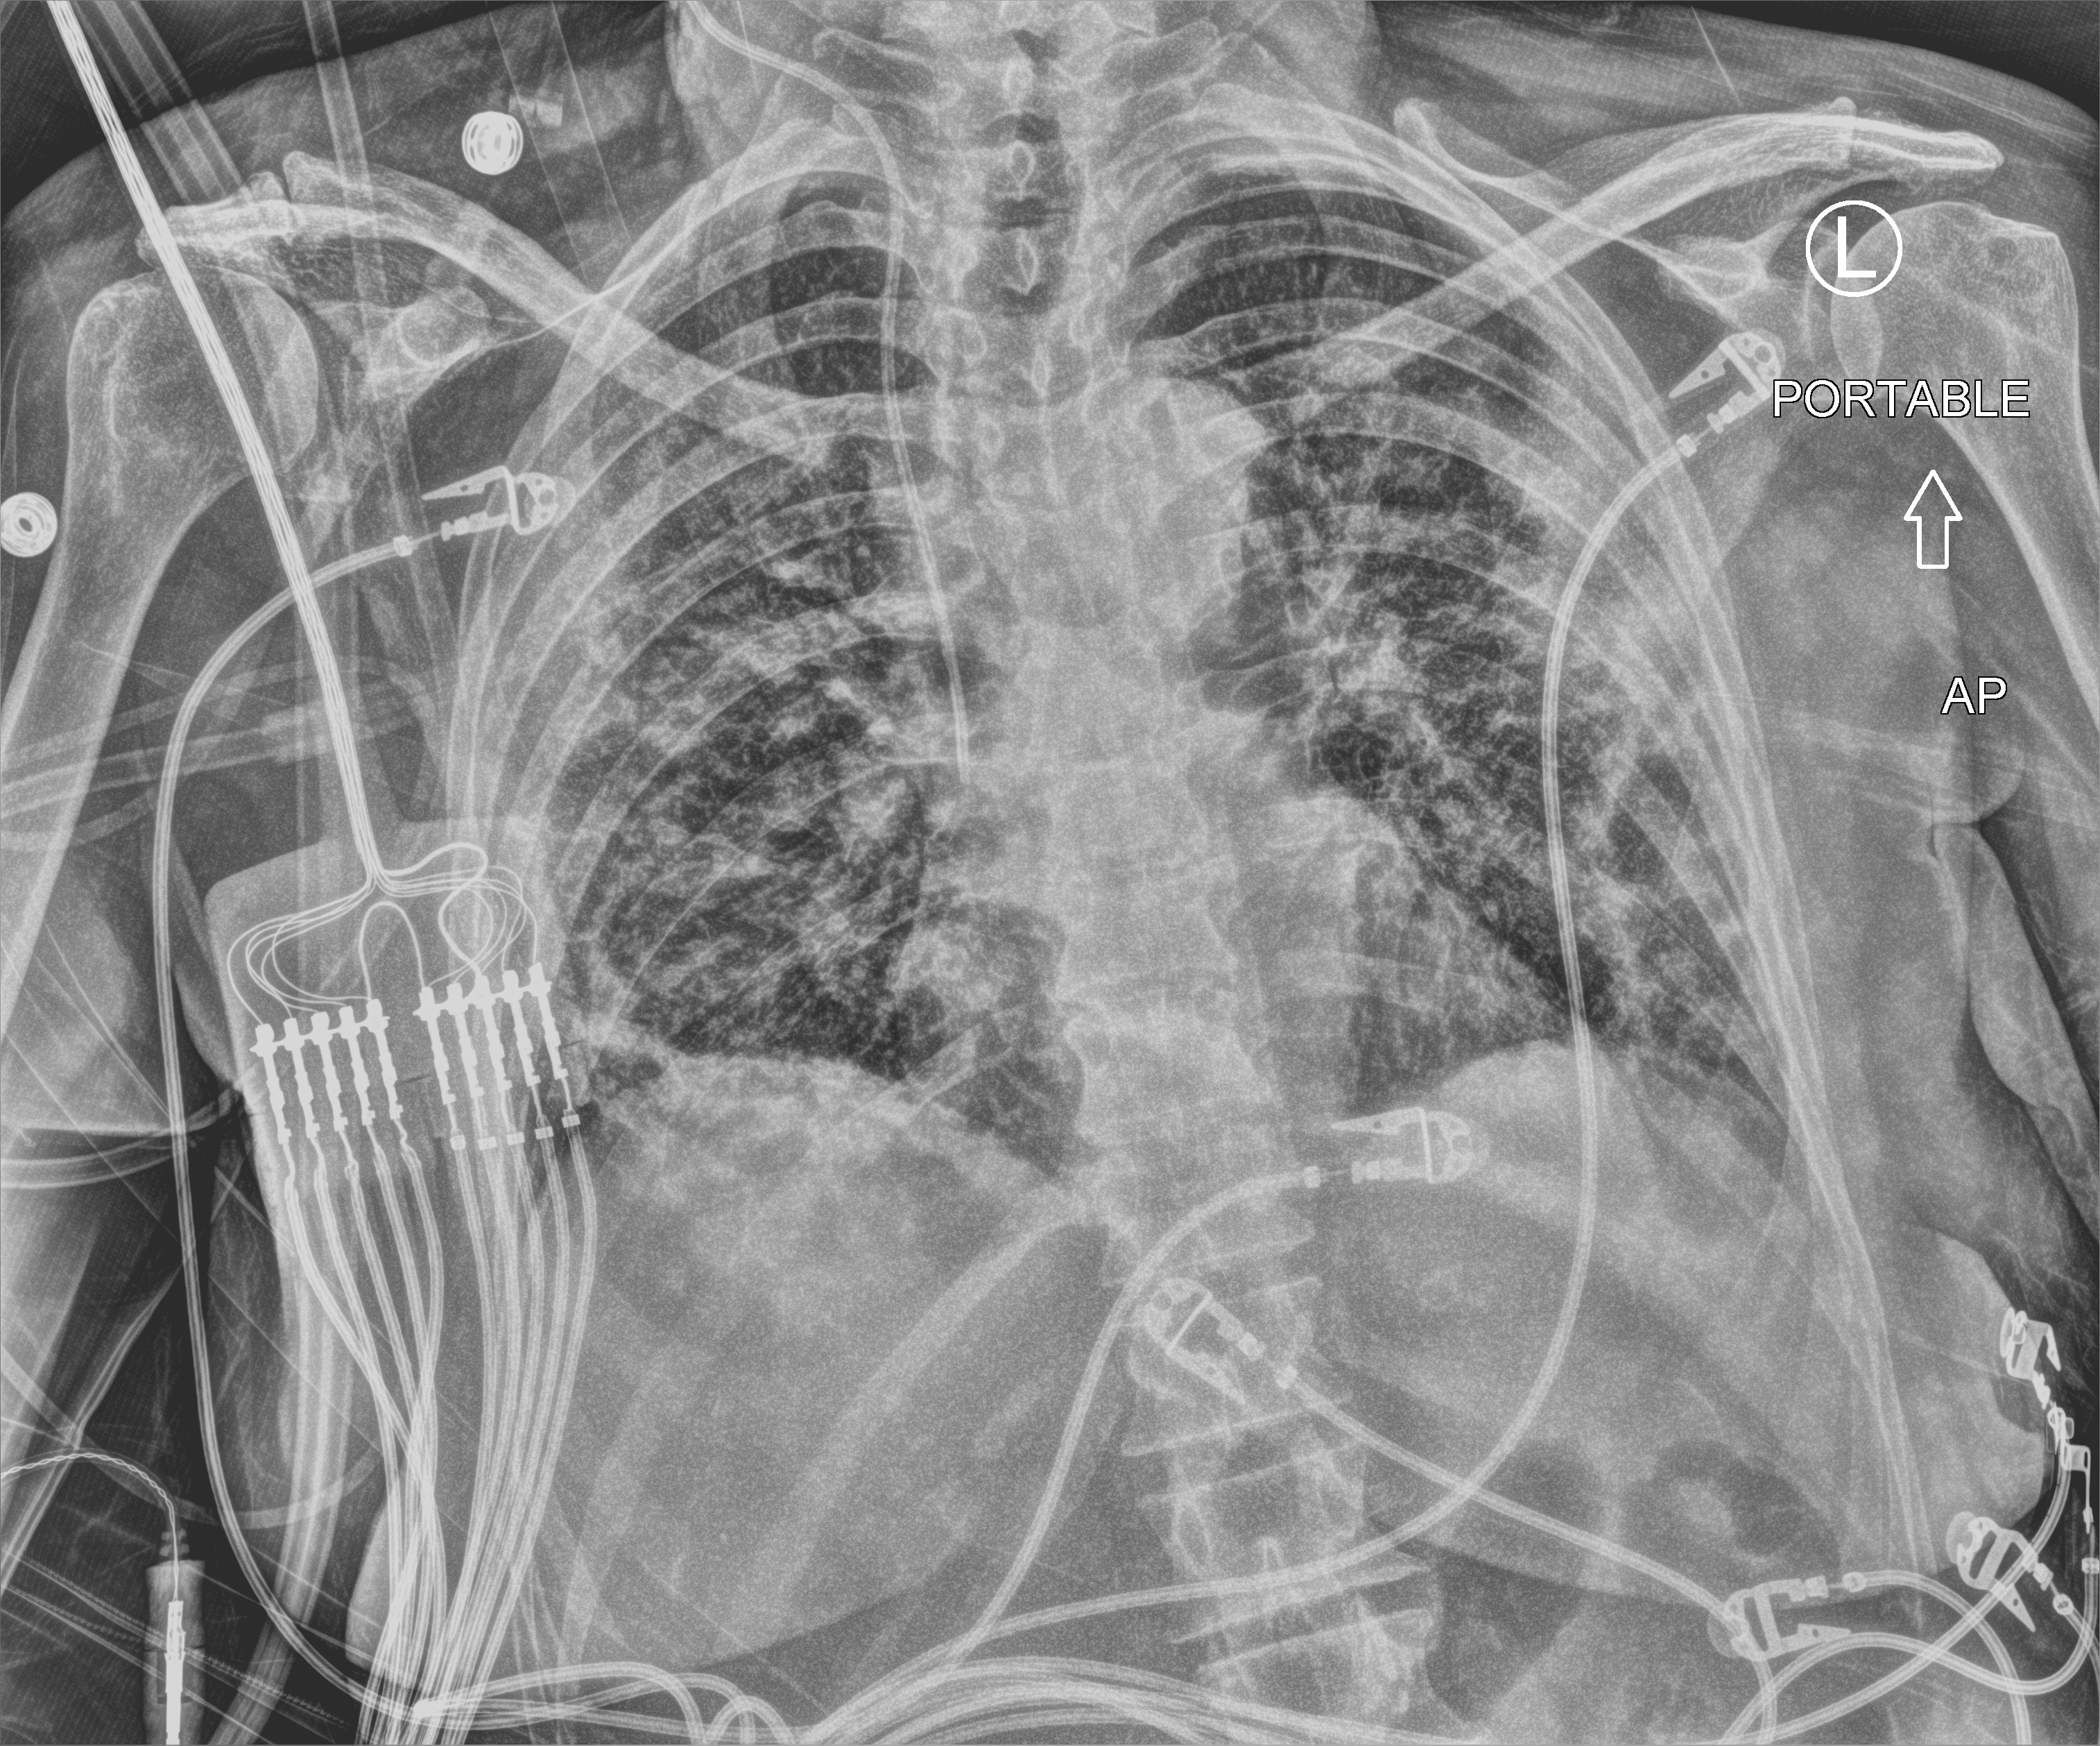
Portable chest radiograph; anteroposterior (AP) projection. Female patient hospitalised with COVID-19, age 60–74 years.
Admission-level facts for this patient (not findings on this image; timing relative to this image not recorded): COPD (admission record): no.